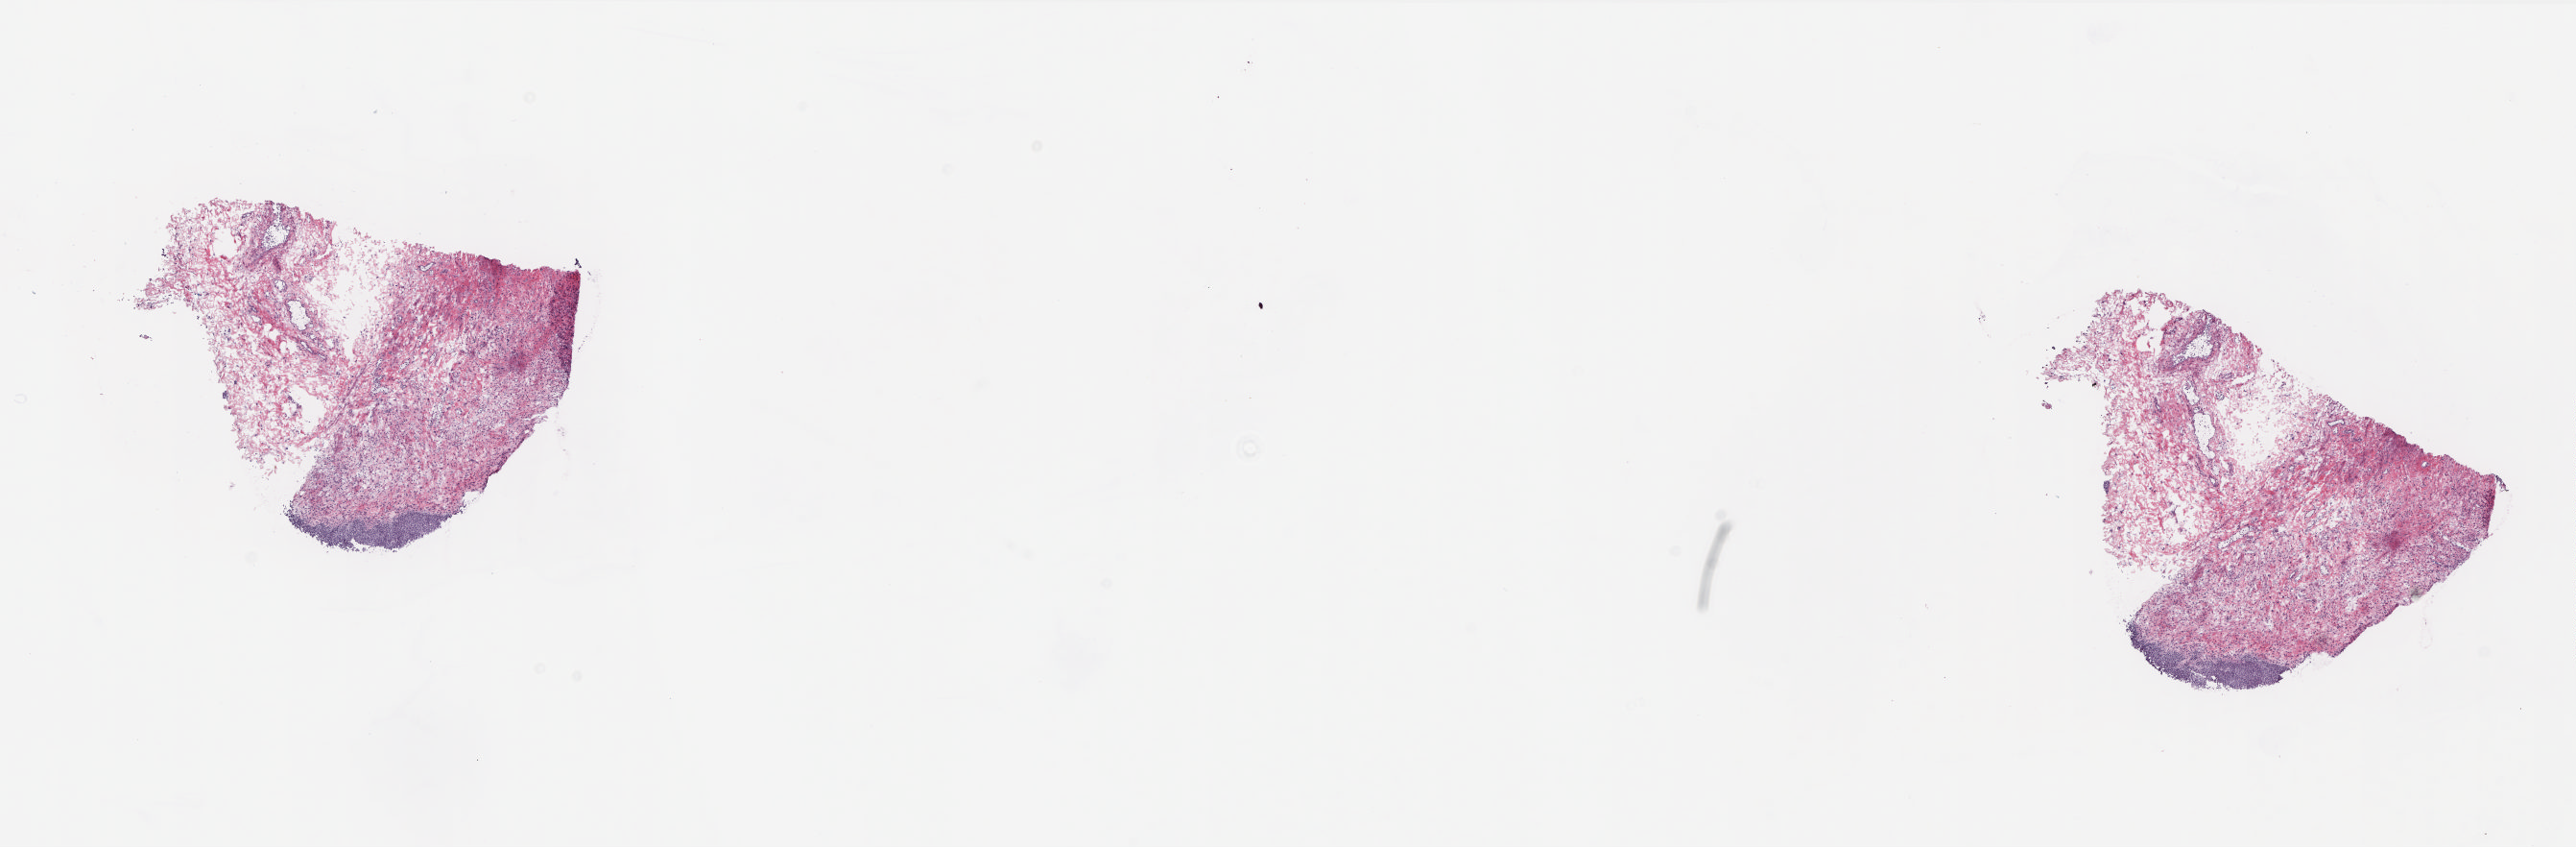
Digitized Hematoxylin and eosin (H&E) stained tissue section (whole slide), a low-resolution overview of the entire scanned area, about 21.6 x 7.1 mm (from a 20x scan); frozen section from the top of the tissue portion; solid tissue normal (non-tumour tissue) sample from the bladder. Female, age 80 years at initial diagnosis. Slide review estimates, as recorded: tumour cells 0%, tumour nuclei 0%, normal cells 25%, stromal cells 75%, necrosis 0%. Infiltration values recorded for this section: lymphocyte infiltration 3%, monocyte infiltration 2%, neutrophil infiltration 3%.
This section: solid tissue normal (non-tumour) sample from the same patient. Patient diagnosis: Transitional cell carcinoma (posterior wall of bladder).